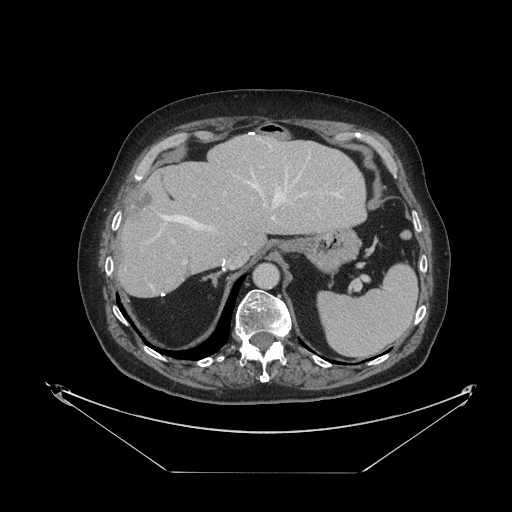
Contrast-enhanced abdominal CT, one axial slice. Position 79 of 121 along the scan axis. Reconstruction kernel STANDARD. 120 kVp. Intravenous contrast given. Soft-tissue window (W 400 / L 40 HU). 2.5 mm slice thickness. 512 × 512 image matrix. Male patient, age 68 years. Case-level facts recorded for this patient, not image findings: diagnosis: colorectal cancer liver metastases, imaged before liver resection; multiple liver metastases: no; largest metastasis: 4 cm; disease in both lobes: no.
Structures marked on this image (manually delineated by an expert):
- hepatic veins: bounding box (x1, y1, x2, y2) in pixels: (156, 144, 340, 237)
- liver: (120, 136, 365, 297)
- planned liver remnant (the part of the liver to remain after resection): (120, 136, 365, 296)
- portal vein (with intrahepatic branches): (172, 166, 262, 264)
- liver metastasis: (131, 189, 153, 217)